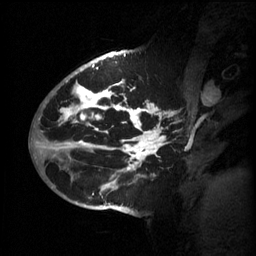
Breast MRI (dynamic contrast-enhanced), one sagittal slice; position 38 of 60 along the scan axis; 3 images stored at this slice position (order not interpretable as contrast timing); 1.5 T; TE 4.2 ms, TR 11 ms; 2 mm slice thickness; 256 × 256 image matrix, field of view 220 × 220 mm. Patient: female, 51 years.
Structures marked on this image (semi-automatically segmented with operator editing):
- analysis volume of interest (the breast-tissue region the enhancement analysis was run in; not a lesion): bounding box (x1, y1, x2, y2) in pixels: (63, 80, 180, 201)
- tumour enhancement mask (voxels above the 70 % enhancement threshold inside the analysis volume of interest): (63, 80, 176, 195)